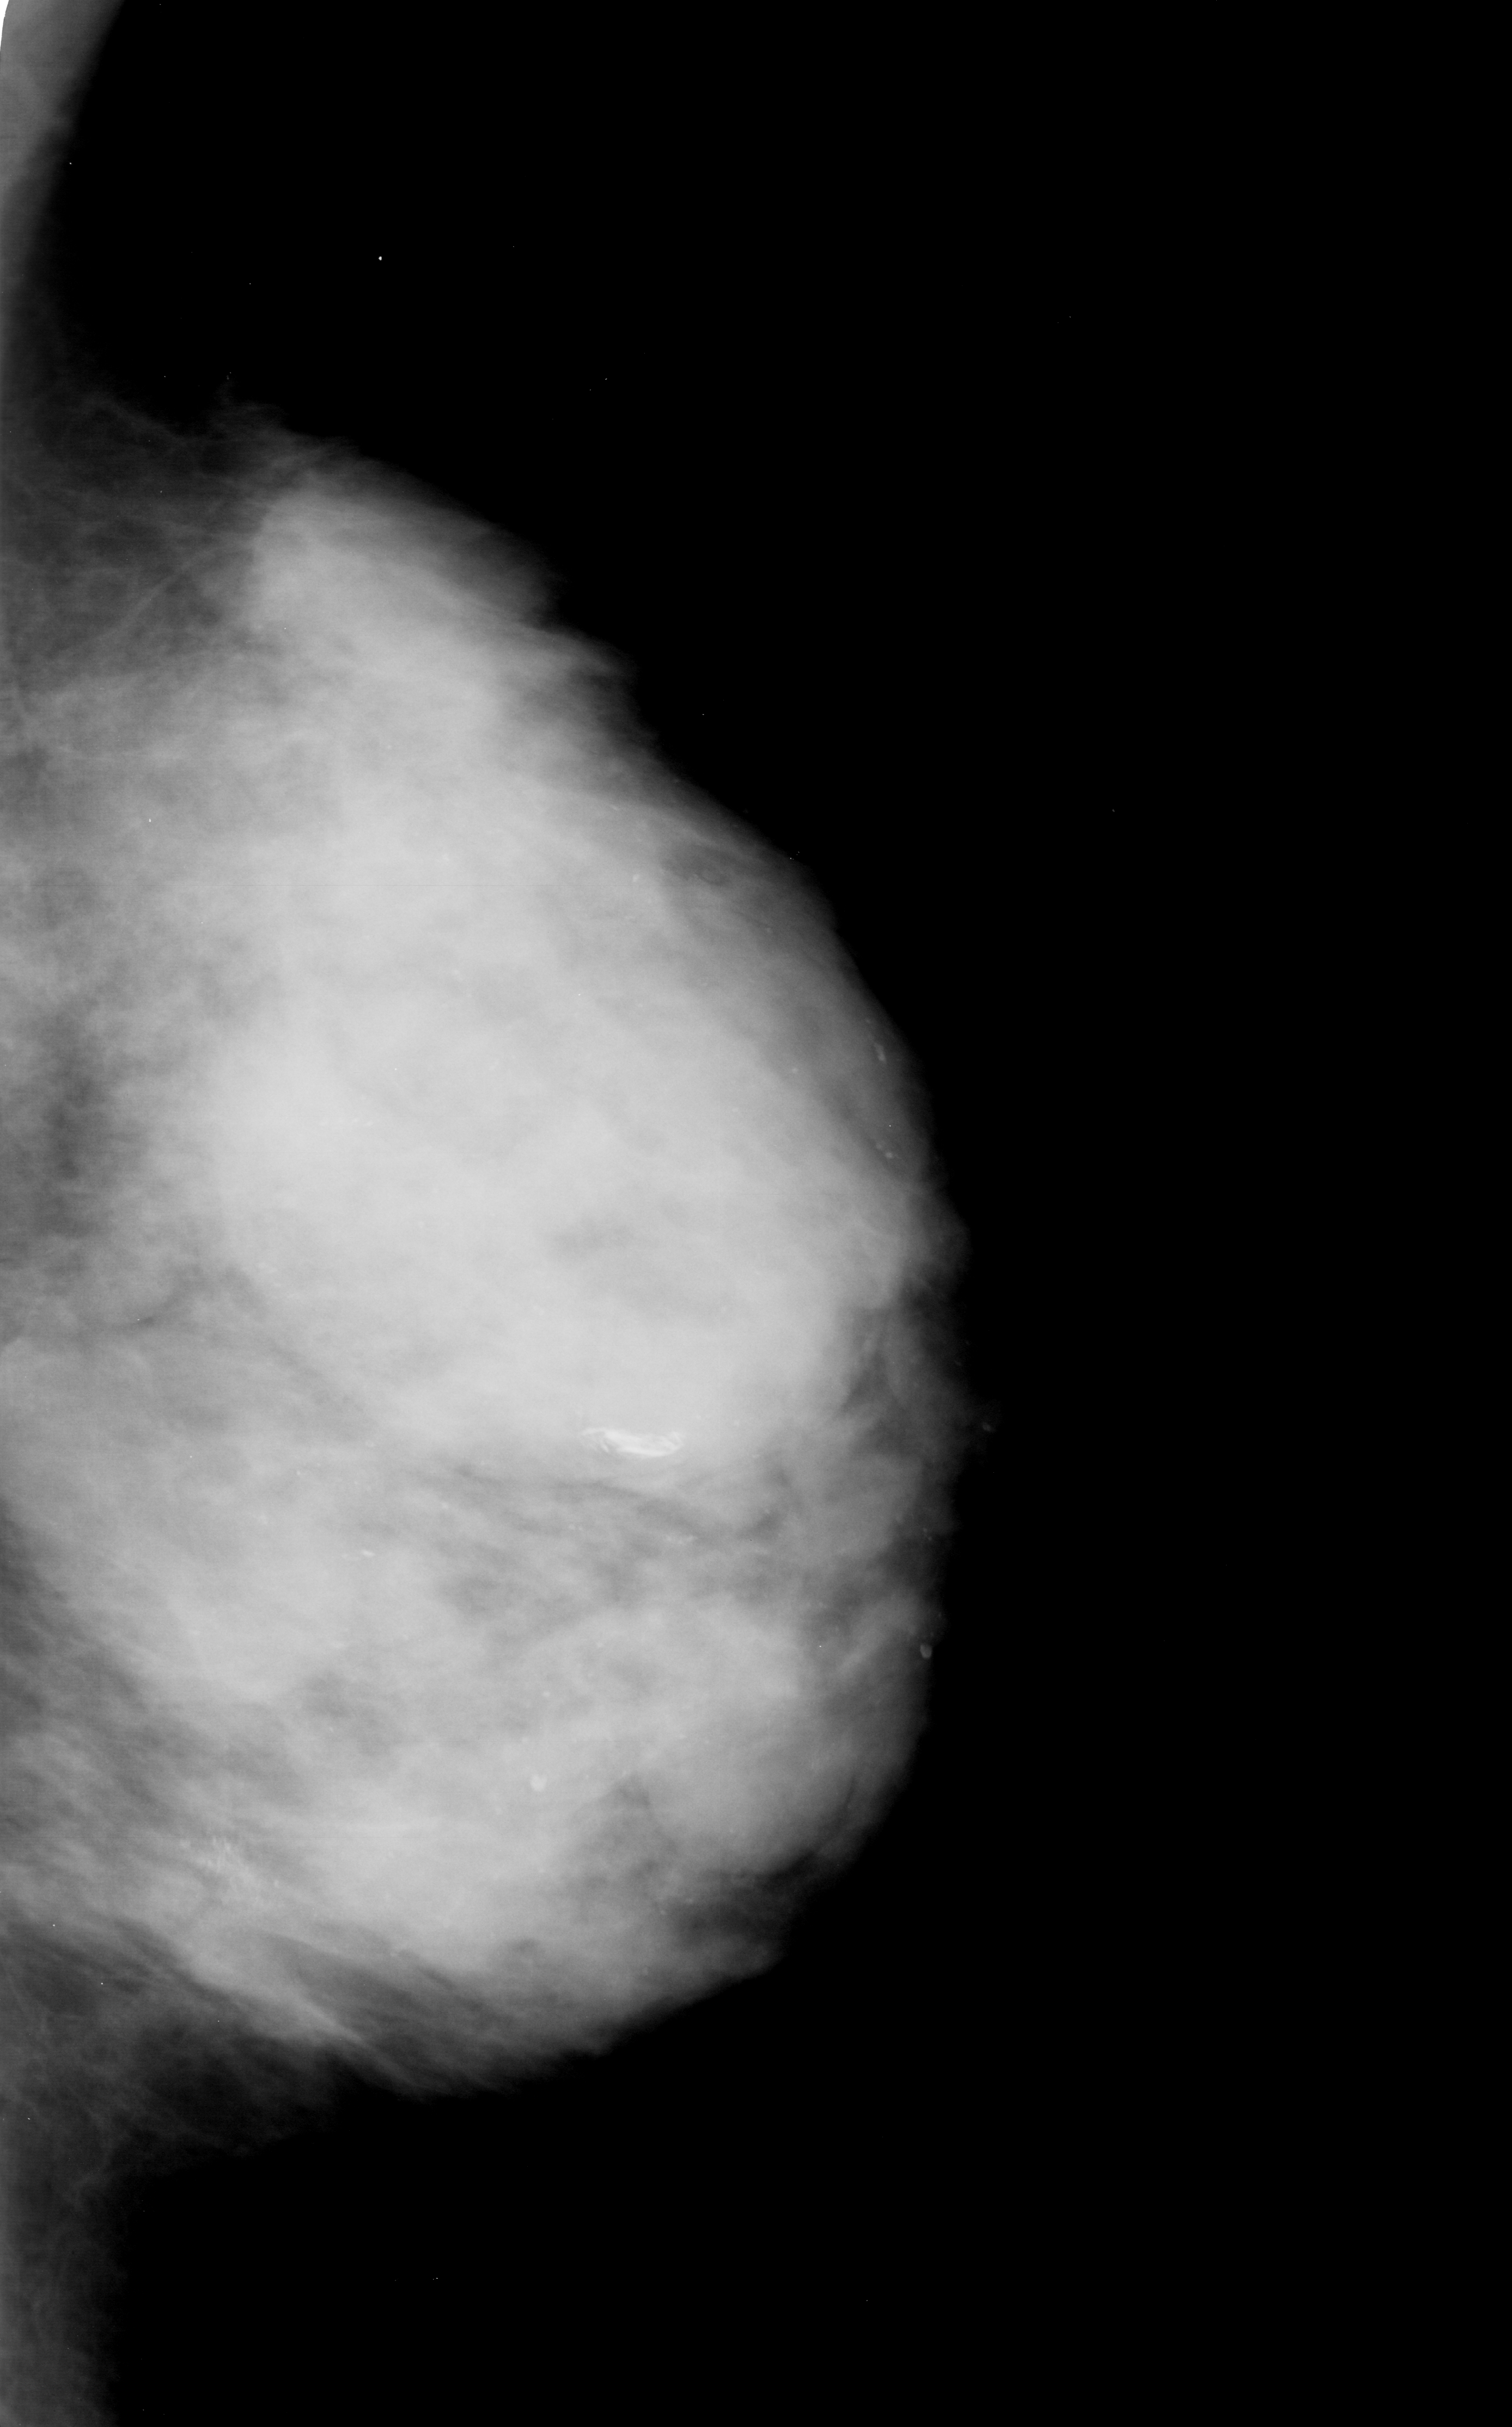
Scanned film-screen mammogram. Left breast. Mediolateral oblique (MLO) view. Breast composition: extremely dense (BI-RADS density category 4 of 4). 1512 × 2427 image matrix.
Expert-marked regions of interest on this image (one box per marked abnormality):
- calcifications, morphology pleomorphic, distribution clustered; BI-RADS assessment category 3; subtlety rating 3 on a 1 (subtle) to 5 (obvious) scale; pathology result (as recorded, not read from the image): malignant: box from (x=108, y=1799) to (x=302, y=1975) px